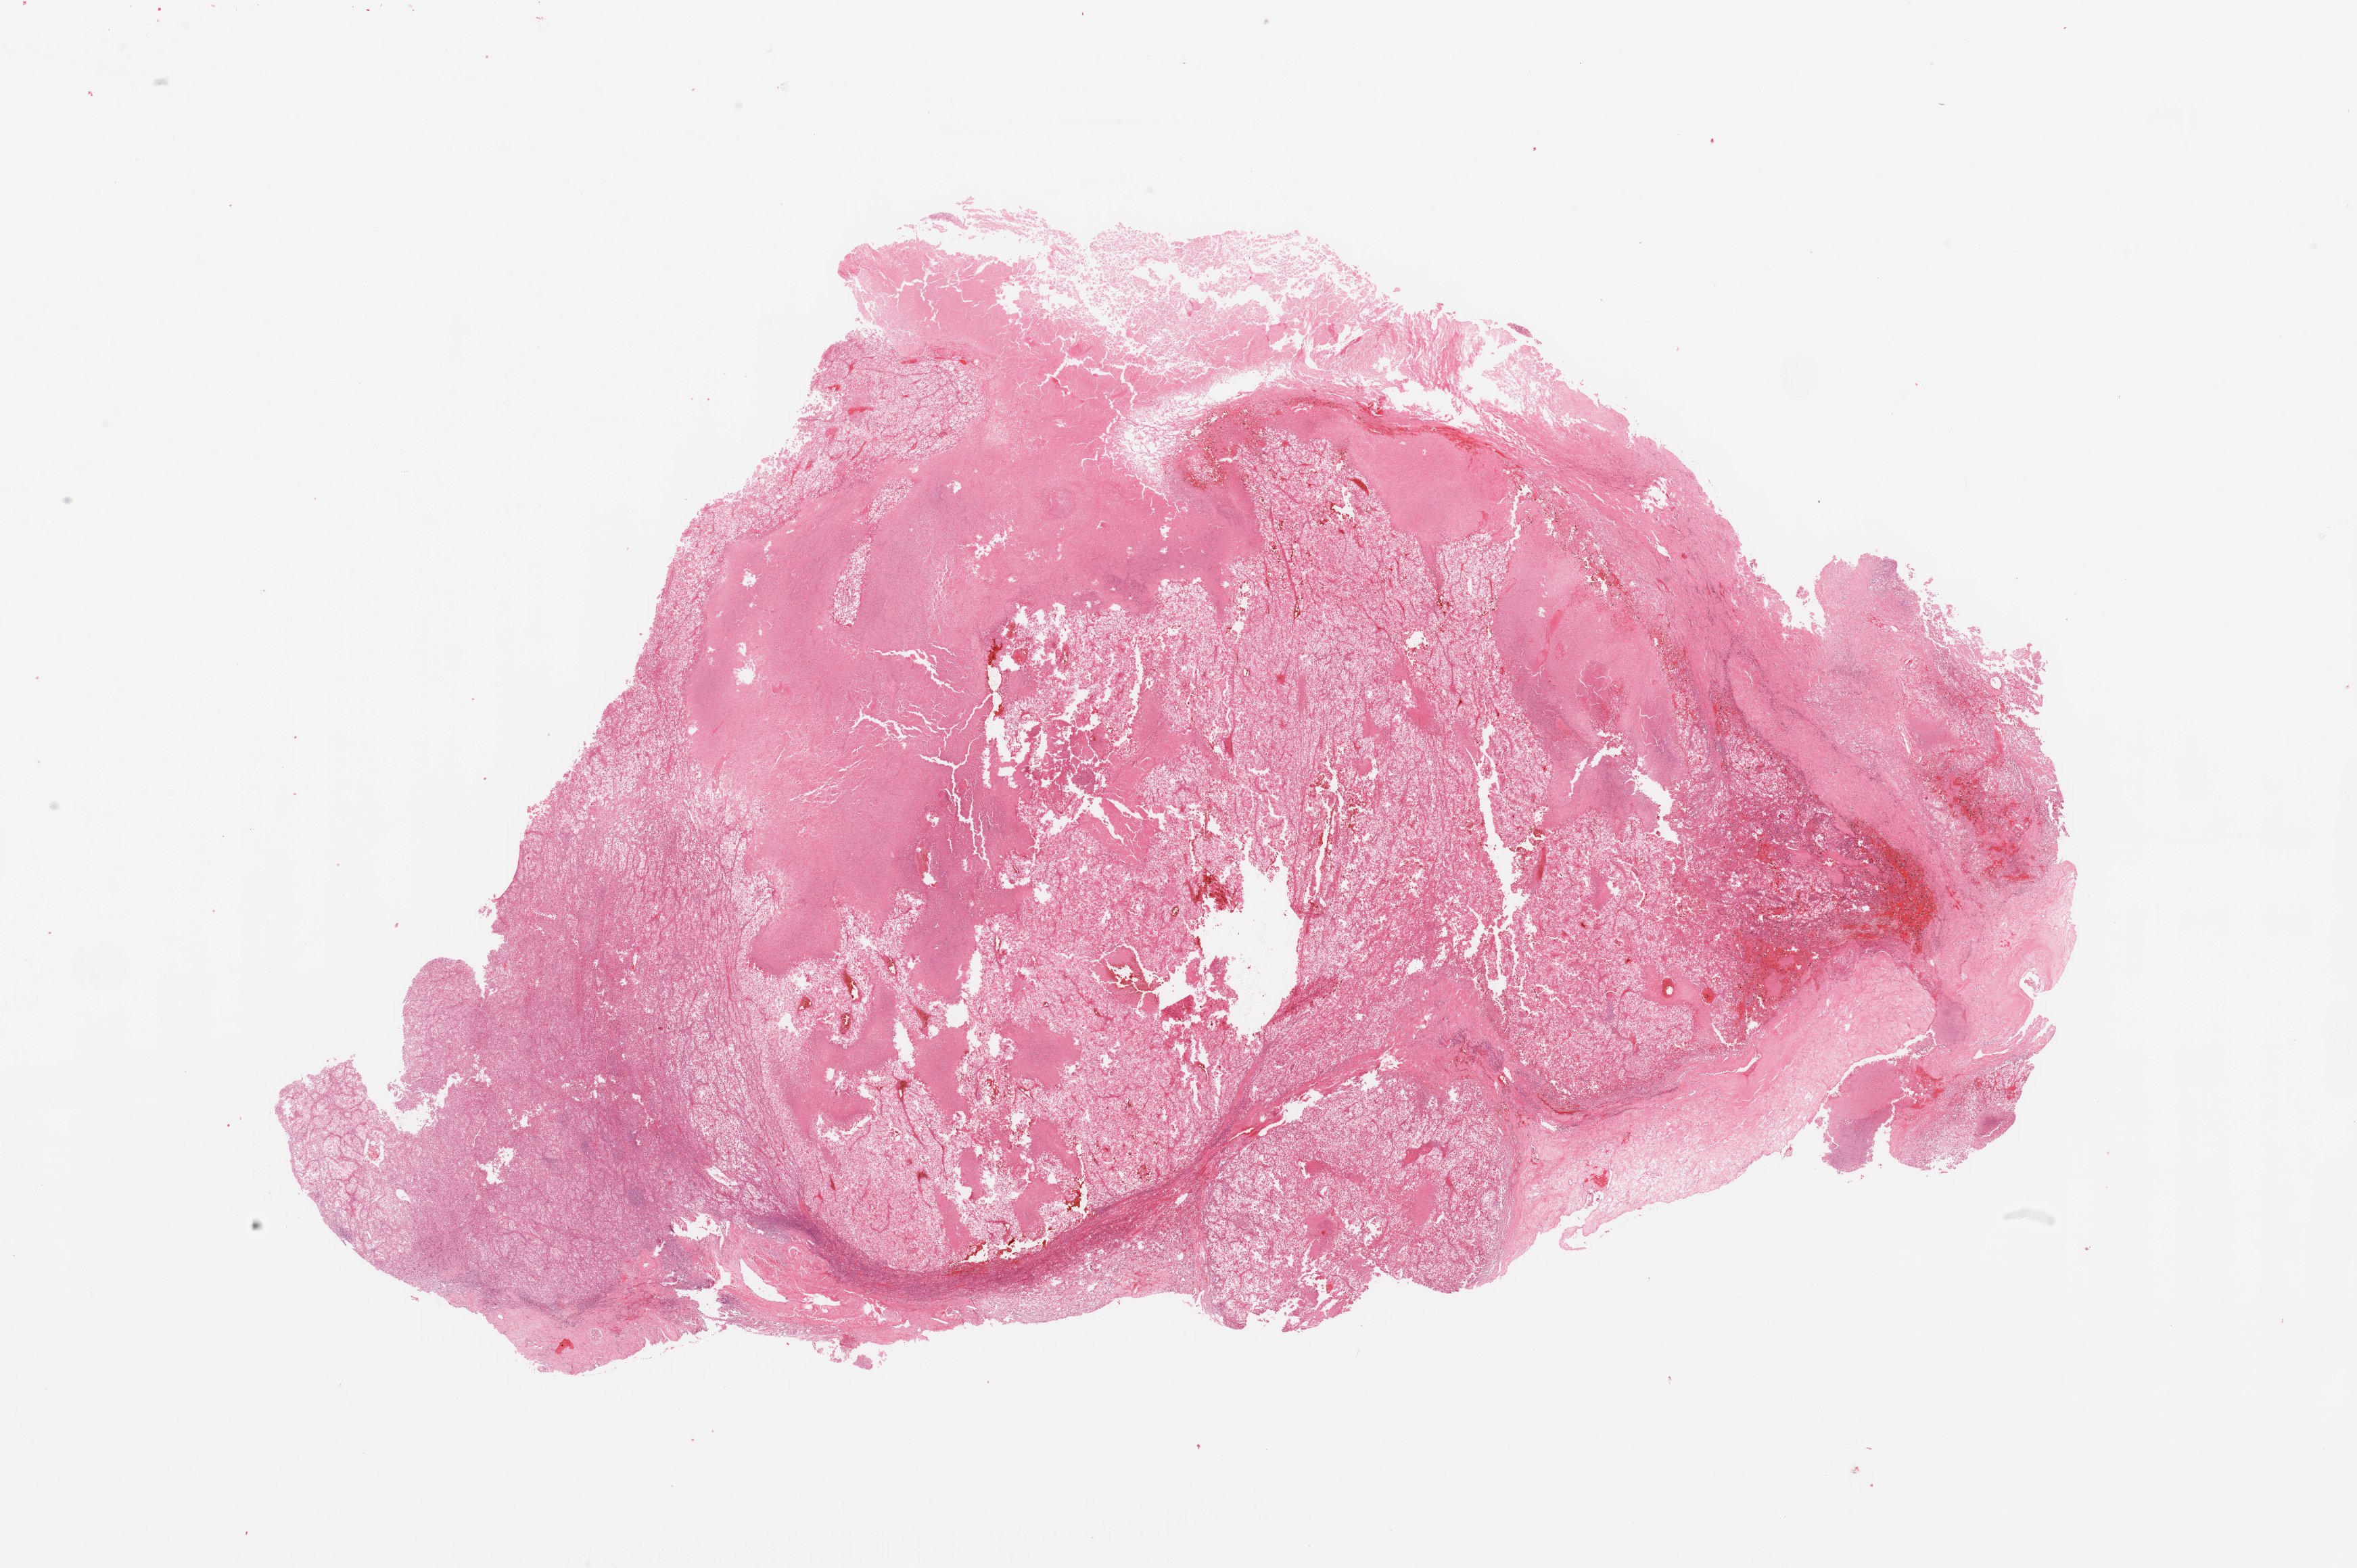
Whole-slide histology image, H&E-stained, low-resolution overview of the scanned area, about 27.6 x 18.3 mm (acquisition: 20x scan); tumour tissue sample, kidney. Patient: female, age 52 years. Histologic grade: G2 (moderately differentiated).
Histologic diagnosis: Renal cell carcinoma, NOS.